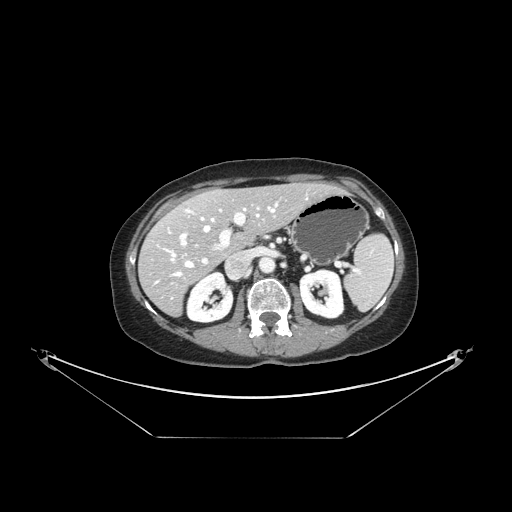
Contrast-enhanced abdominal CT, one axial slice; intravenous contrast given; soft-tissue window (W 400 / L 40 HU); 512 × 512 image matrix, field of view 500 × 500 mm. Female patient, age 73 years. From the clinical record (not read from this slice): diagnosis: colorectal cancer liver metastases, imaged before liver resection; multiple liver metastases: no; largest metastasis: 1 cm; disease in both lobes: no.
Structures marked on this image (outlined manually by an expert reader):
- hepatic veins: box from (x=157, y=204) to (x=277, y=282) px
- liver: (x=141, y=184)–(x=335, y=315)
- planned liver remnant (the part of the liver to remain after resection): (x=168, y=184)–(x=334, y=252)
- portal vein (with intrahepatic branches): (x=179, y=207)–(x=259, y=264)